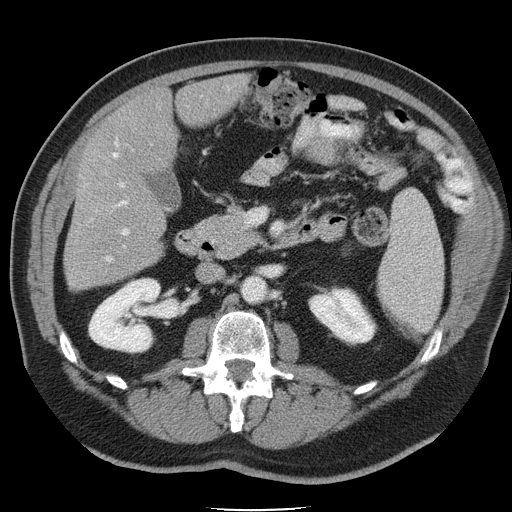
Contrast-enhanced abdominal CT, one axial slice. Position 18 of 45 along the scan axis. Intravenous contrast given. Soft-tissue window (W 400 / L 40 HU). 512 × 512 image matrix, field of view 386 × 386 mm. Male patient, age 65 years. From the clinical record (not read from this slice): diagnosis: colorectal cancer liver metastases, imaged before liver resection; multiple liver metastases: yes; largest metastasis: 4.9 cm; disease in both lobes: no.
Structures marked on this image (expert manual segmentation):
- hepatic veins: bounding box (x1, y1, x2, y2) in pixels: (105, 153, 118, 262)
- liver: (64, 76, 246, 289)
- planned liver remnant (the part of the liver to remain after resection): (94, 76, 246, 173)
- portal vein (with intrahepatic branches): (117, 183, 129, 235)